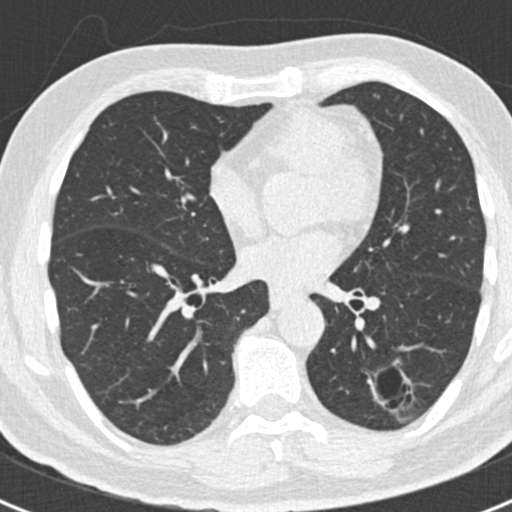
Low-dose screening chest CT, axial slice, first (baseline) screen, lung window (W 1500 / L -600 HU), standard (soft-tissue) reconstruction kernel (B30f), slice 93 of 188 in the series, 512 × 512 image matrix, field of view 300 × 300 mm. Male, age 66 years at enrolment. Former smoker at enrolment.
Lesion marked by an expert reader, box from (x=347, y=342) to (x=422, y=421) px. The exam's reader record, not a measurement of the box and not confirmed to be the same lesion: non-calcified nodule or mass ≥4 mm, left lower lobe, 43 × 27 mm, smooth margins. Official screen result: positive, change unspecified: nodule(s) >= 4 mm or enlarging nodule(s), mass(es), or other non-specific abnormalities suspicious for lung cancer. Participant outcome: lung cancer diagnosed 801 days after this screen — adenocarcinoma, NOS, left lower lobe, poorly differentiated (G3), stage IB (AJCC 6th edition), 38 mm at pathology.